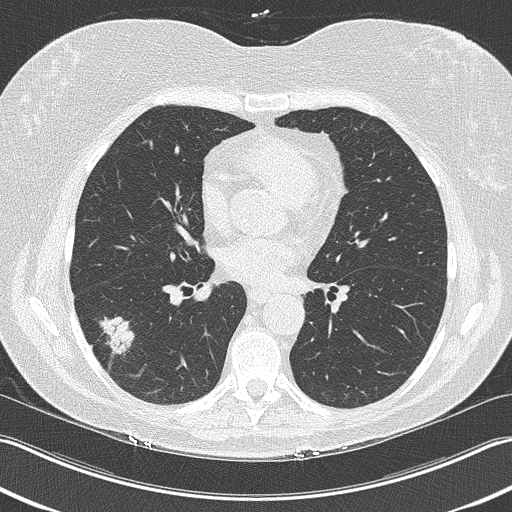
Low-dose screening chest CT, one axial slice. Position 113 of 210 along the scan axis. Reconstruction kernel B50f. 120 kVp. Lung window (W 1500 / L -600 HU). 512 × 512 image matrix, field of view 348 × 348 mm.
Outlined on this slice (expert manual segmentation):
- lesion 1 (tumor, lower lobe of right lung): bounding box <99,316,135,358> (left, top, right, bottom; pixels)